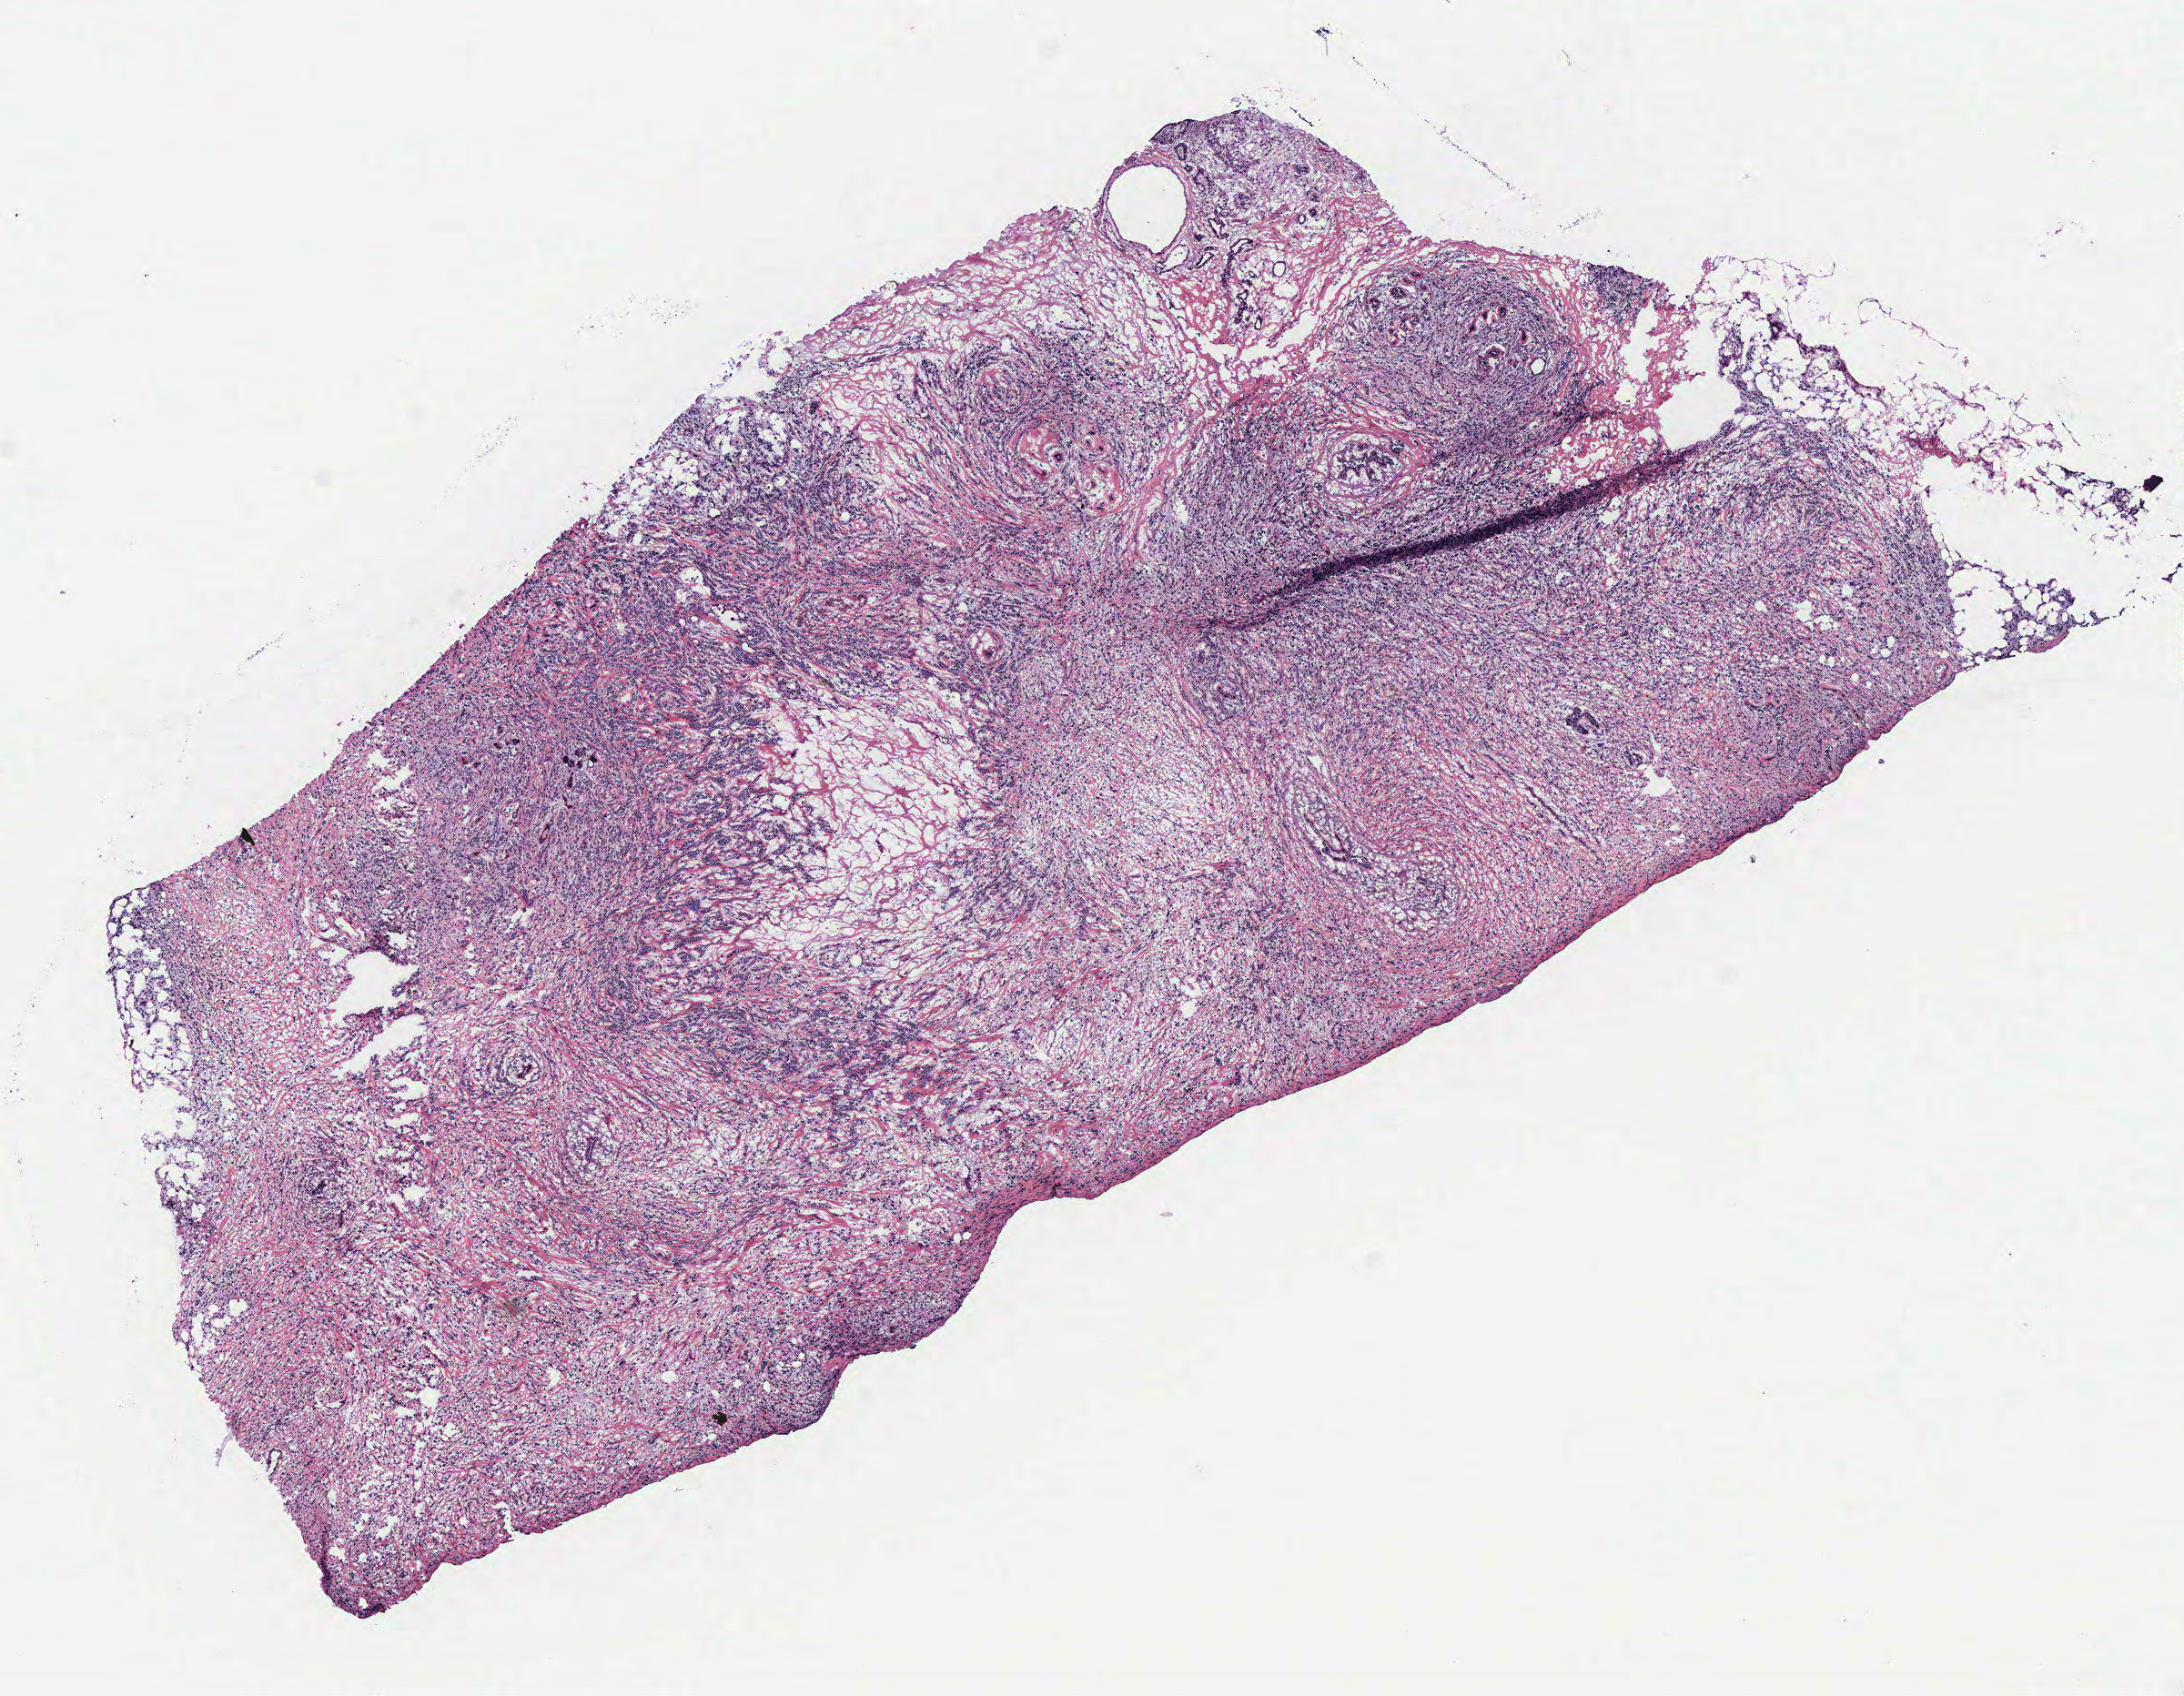
Whole-slide histology image, H&E-stained — low-resolution overview of the scanned area, about 9.6 x 7.5 mm. 46-year-old female patient.
• specimen: breast, tumour tissue